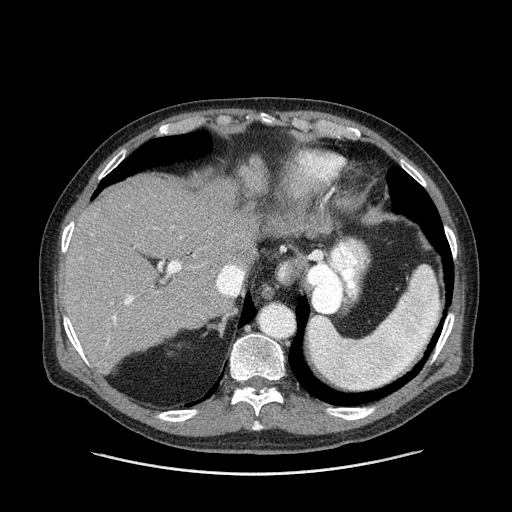
Contrast-enhanced abdominal CT (liver protocol), one axial slice. Slice 108 of 180 in the series (ordered by position). Reconstruction kernel STANDARD. One of 2 acquisitions stored at this slice position. Soft-tissue window (W 400 / L 40 HU). 2.5 mm slice thickness. 512 × 512 image matrix, field of view 420 × 420 mm. From the clinical record (not read from this slice): diagnosis: hepatocellular carcinoma (patient treated with transarterial chemoembolisation; whether this scan precedes or follows treatment is not stated here); TNM stage (as recorded): Stage-II; Child-Pugh class: A; tumour size: 2.8 cm.
Structures marked on this image (semi-automatic segmentation, software-assisted and operator-edited):
- liver parenchyma outside the tumour (the mass and vessels are separate outlines, so this box may not span the whole liver): box from (x=64, y=158) to (x=266, y=372) px
- liver vessels: (x=80, y=260)–(x=181, y=351)